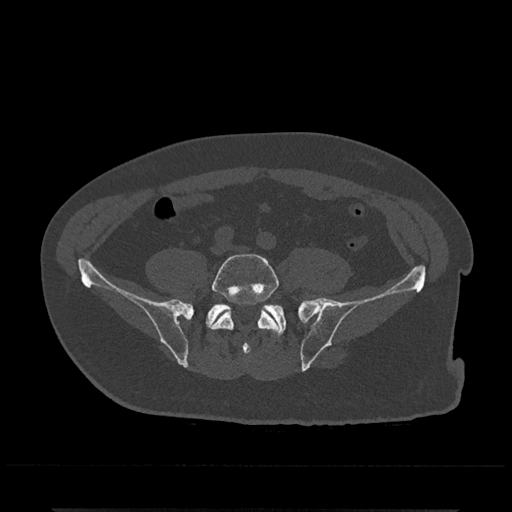
CT including the spine, one axial slice. Position 69 of 797 along the scan axis. Bone window (W 1800 / L 400 HU). 0.5 mm slice thickness. 512 × 512 image matrix, field of view 393 × 393 mm. Male patient, age 67 years. From the clinical record (not read from this slice): primary cancer: prostate.
Structures marked on this image (semi-automatically segmented with operator editing):
- L5 vertebra: bounding box (x1, y1, x2, y2) in pixels: (210, 253, 279, 353)